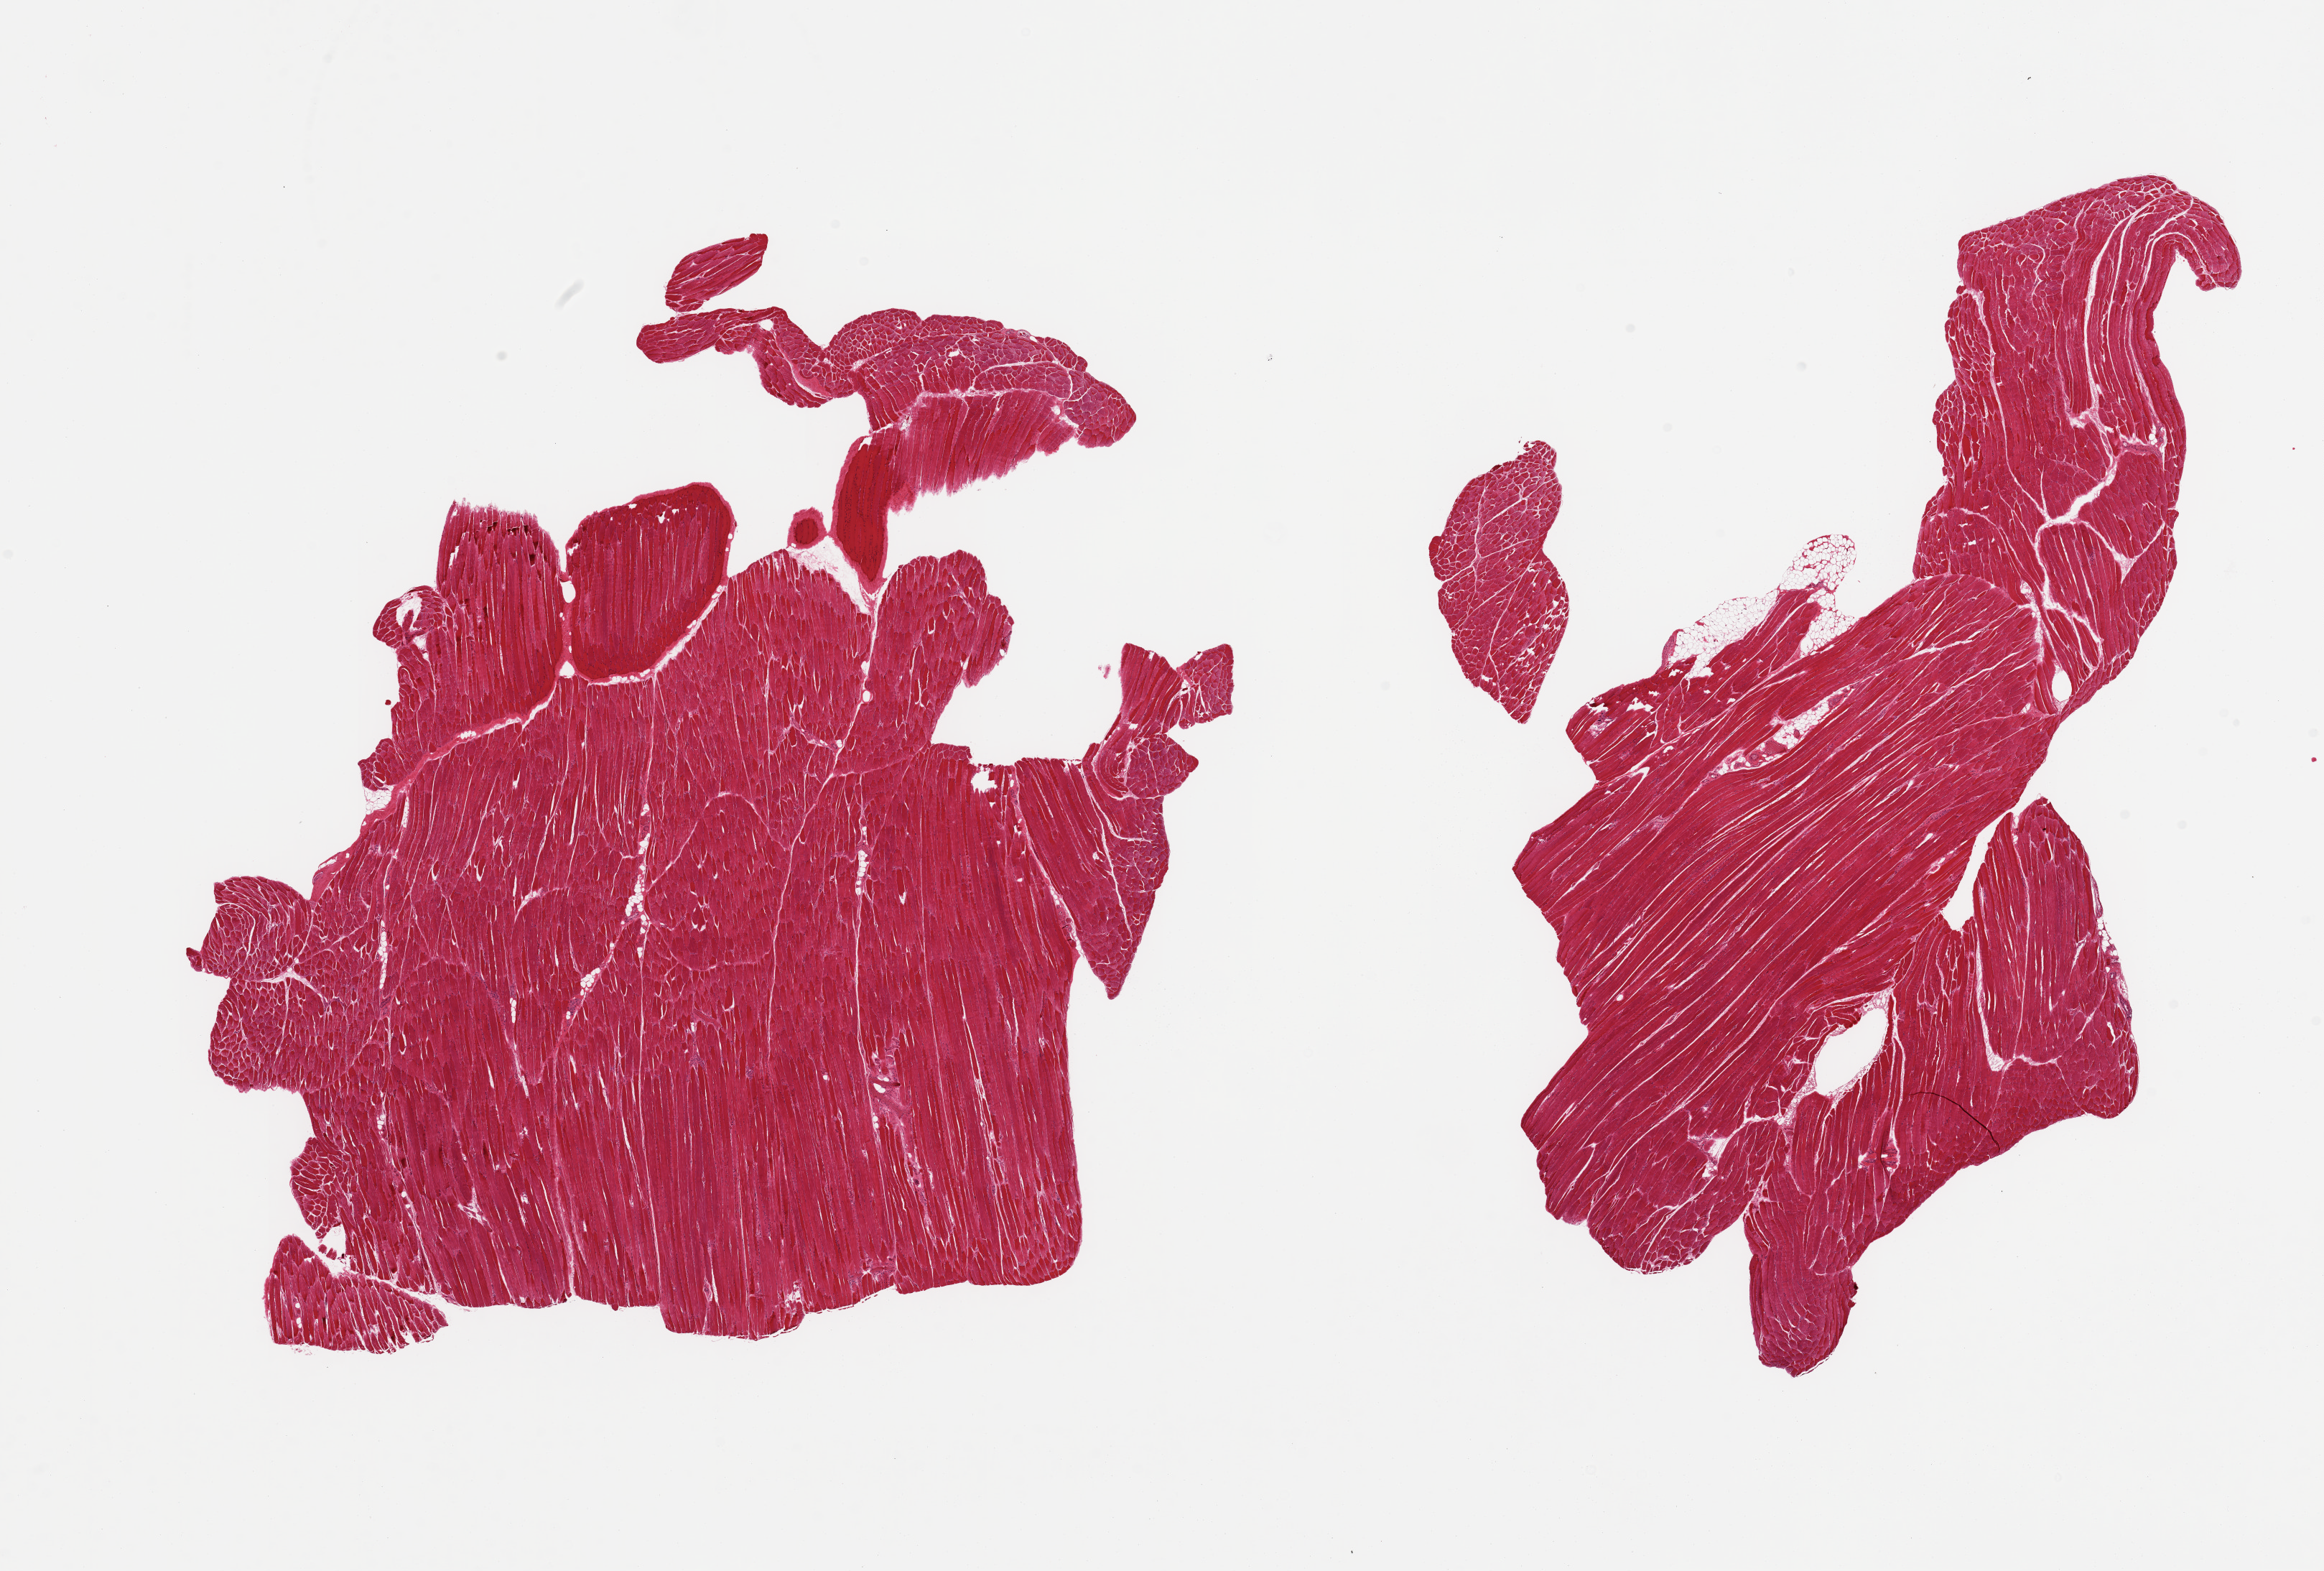
Haematoxylin and eosin whole-slide image, low-resolution overview of the scanned area, about 25.6 x 17.3 mm; PAXgene-fixed paraffin-embedded (PFPE) section; target tissue: skeletal muscle; donor tissue sample. Male donor.
Reviewer comment on this tissue sample: 2 pieces <5% interstitial fat.